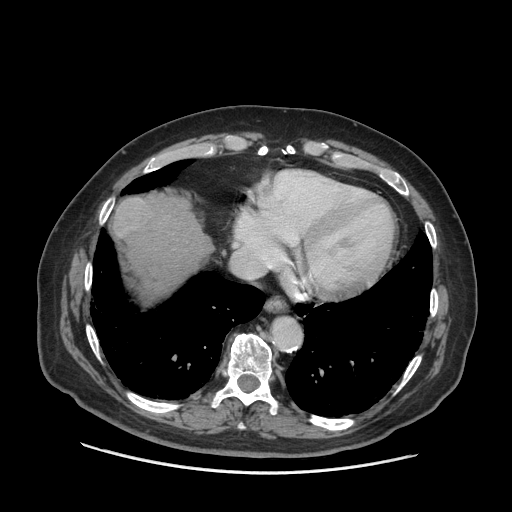
Contrast-enhanced abdominal CT (liver protocol), one axial slice; reconstruction kernel STANDARD; 140 kVp; soft-tissue window (W 400 / L 40 HU); 2.5 mm slice thickness; 512 × 512 image matrix, field of view 420 × 420 mm. Case-level facts recorded for this patient, not image findings: diagnosis: hepatocellular carcinoma (patient treated with transarterial chemoembolisation; whether this scan precedes or follows treatment is not stated here); TNM stage (as recorded): Stage-I.
Outlined on this slice (semi-automatic segmentation, software-assisted and operator-edited):
- abdominal aorta: bounding box [x1, y1, x2, y2] px = [272, 319, 301, 348]
- liver parenchyma outside the tumour (the mass and vessels are separate outlines, so this box may not span the whole liver): [112, 196, 210, 298]
- mass: [113, 198, 152, 238]